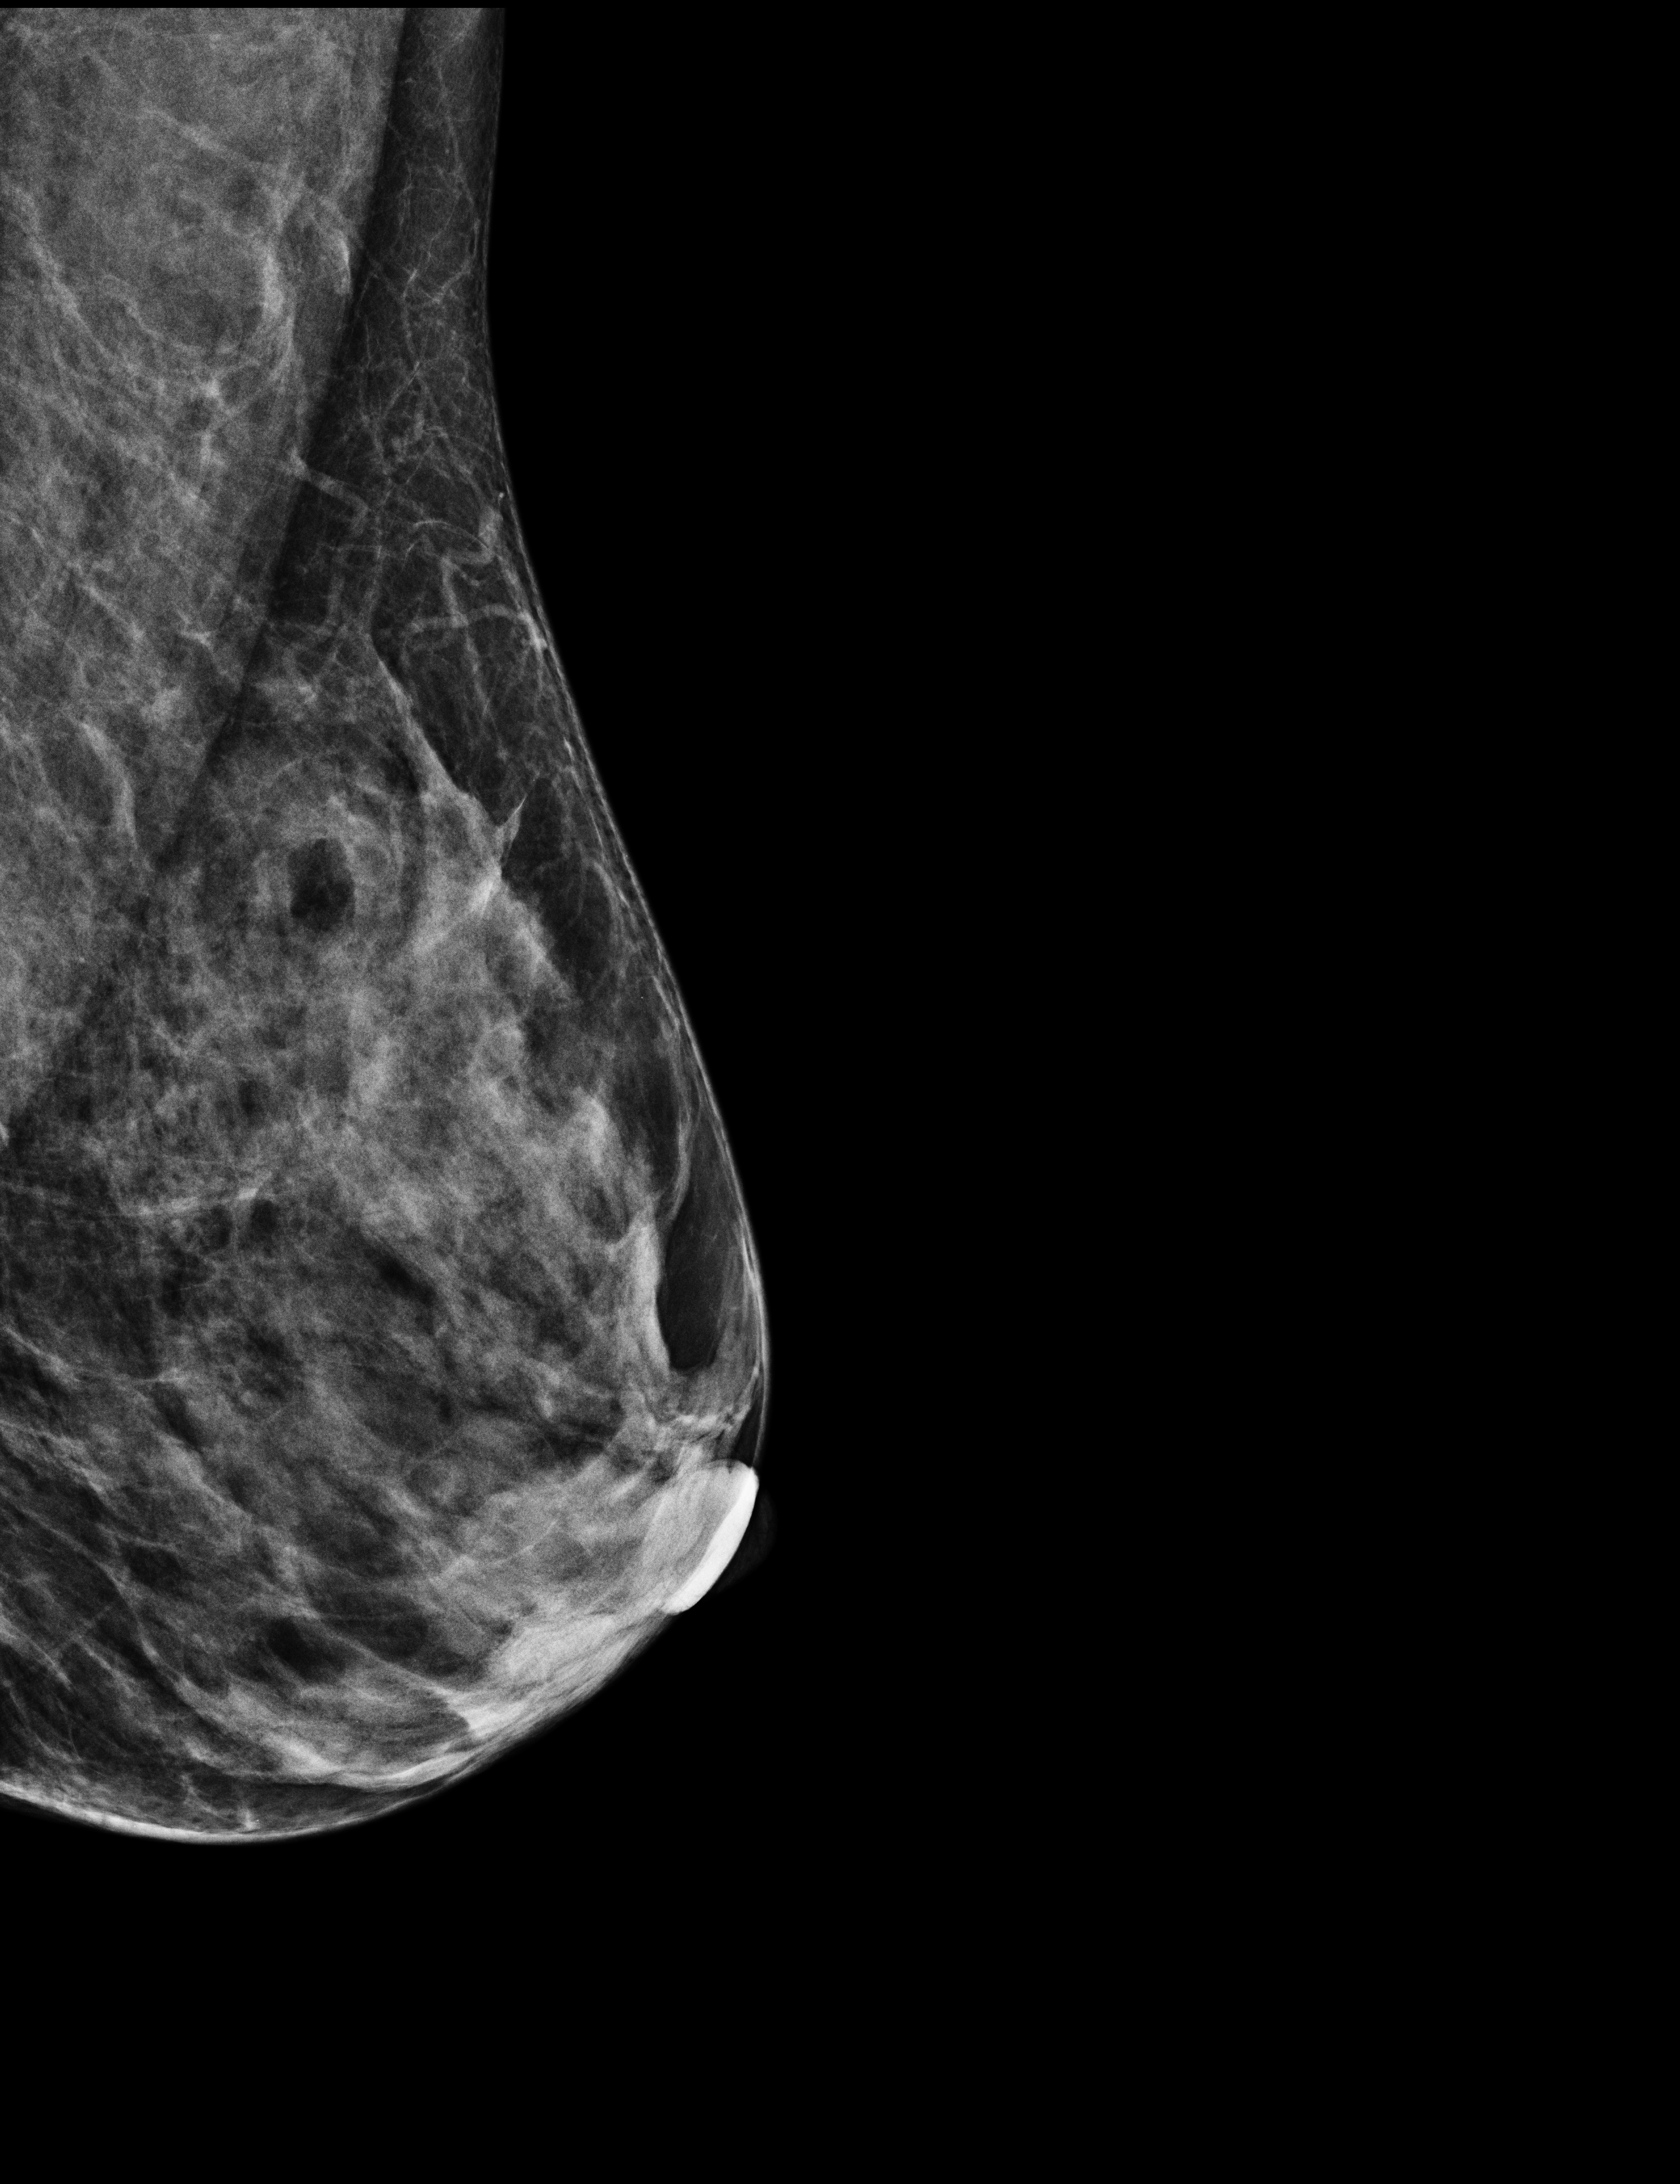
Annual screening mammography examination; system: Selenia Dimensions. Female patient, age 55 years.
Image type: full-field digital mammogram. Breast: left. Projection: medio-lateral oblique projection. Breast density at the screening exam (both breasts): heterogeneously dense (BI-RADS density category c). Final BI-RADS assessment for this screening round (tomosynthesis exam, both breasts): category 2. Recall: no recall after this screen.